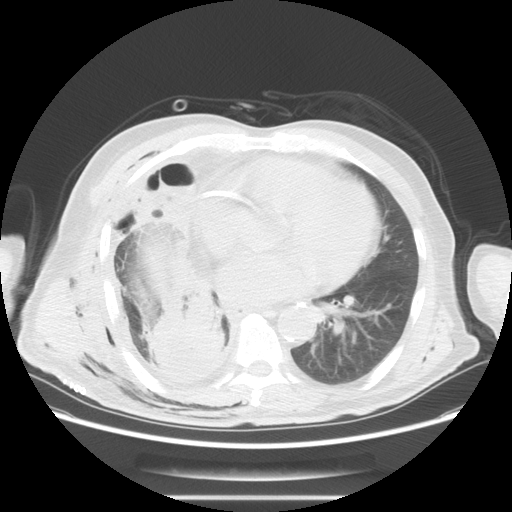
Chest CT, one axial slice. Slice 28 of 59 in the series (ordered by position). Lung window (W 1500 / L -600 HU). 5 mm slice thickness. 512 × 512 image matrix, field of view 392 × 392 mm. Male patient, age 69 years. From the clinical record (not read from this slice): clinical TNM (as recorded): T3 N0 M0; histopathological grade: G2-3.
Outlined on this slice (rectangle marked by the reading radiologist):
- lung tumour (recorded histology: squamous cell carcinoma): bounding box [x1, y1, x2, y2] px = [142, 289, 242, 400]